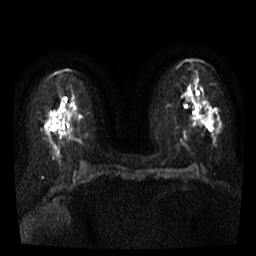
Breast MRI, one axial slice; position 15 of 35 along the scan axis; diffusion-weighted series; image 2 of 4 stored at this slice position (different b-values; order by instance number); 3 T; 5 mm slice thickness; 256 × 256 image matrix. Female patient.
Annotated regions visible in this slice (expert manual segmentation):
- tumour on diffusion-weighted imaging: box from (x=203, y=115) to (x=210, y=125) px